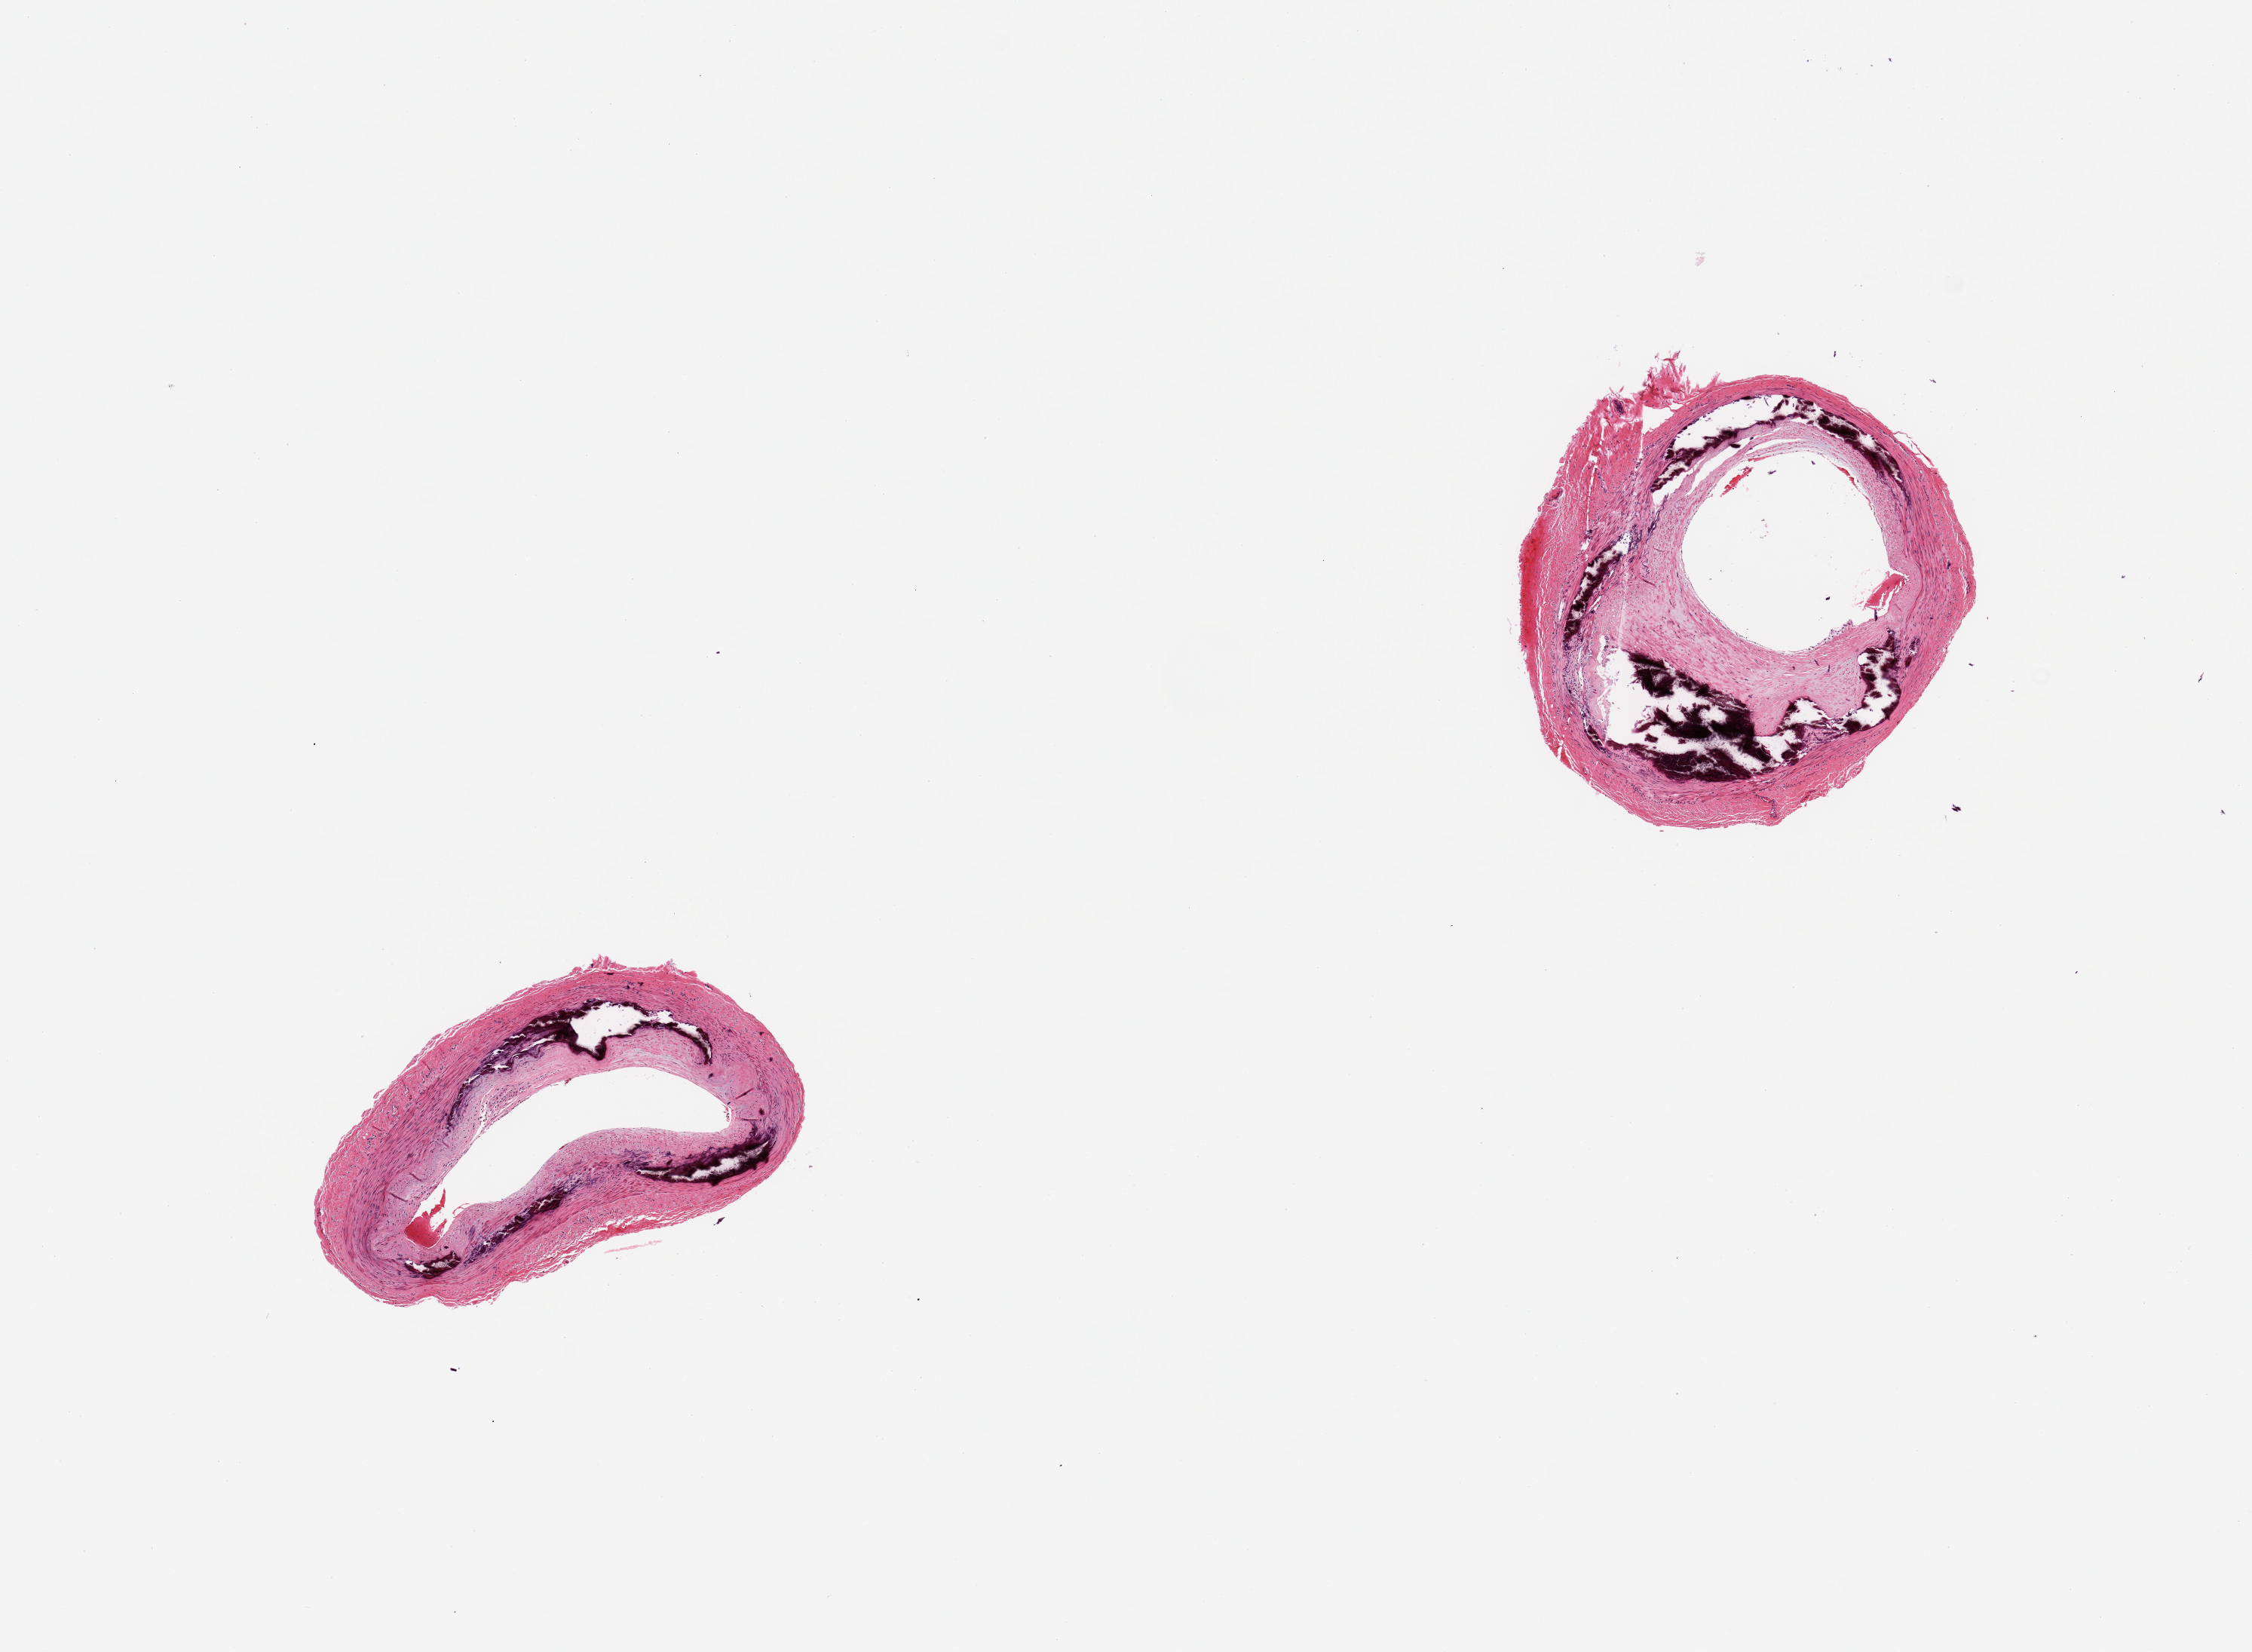
Whole-slide image, haematoxylin and eosin stain — low-resolution overview of the scanned area, about 11.8 x 8.7 mm. PAXgene-fixed paraffin-embedded (PFPE) section. Section of tibial artery (target tissue). Tissue donor sample. Female donor.
* review note (as recorded): 2 pieces; severe medial calcification; moderate intimal fibrous sclerosis